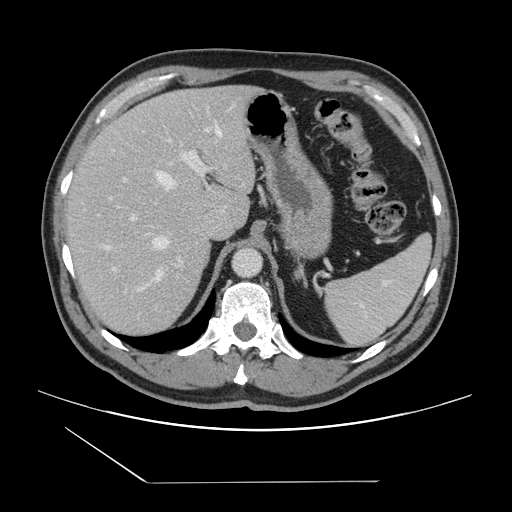
Contrast-enhanced abdominal CT, one axial slice; 120 kVp; soft-tissue window (W 400 / L 40 HU); 2.5 mm slice thickness; 512 × 512 image matrix. Male patient, age 61 years. From the clinical record (not read from this slice): diagnosis: colorectal cancer liver metastases, imaged before liver resection; multiple liver metastases: yes; largest metastasis: 5.5 cm.
Outlined on this slice (manually delineated by an expert):
- hepatic veins: box from (x=154, y=129) to (x=222, y=279) px
- liver: (x=68, y=86)–(x=256, y=336)
- planned liver remnant (the part of the liver to remain after resection): (x=68, y=86)–(x=238, y=229)
- portal vein (with intrahepatic branches): (x=105, y=127)–(x=210, y=263)